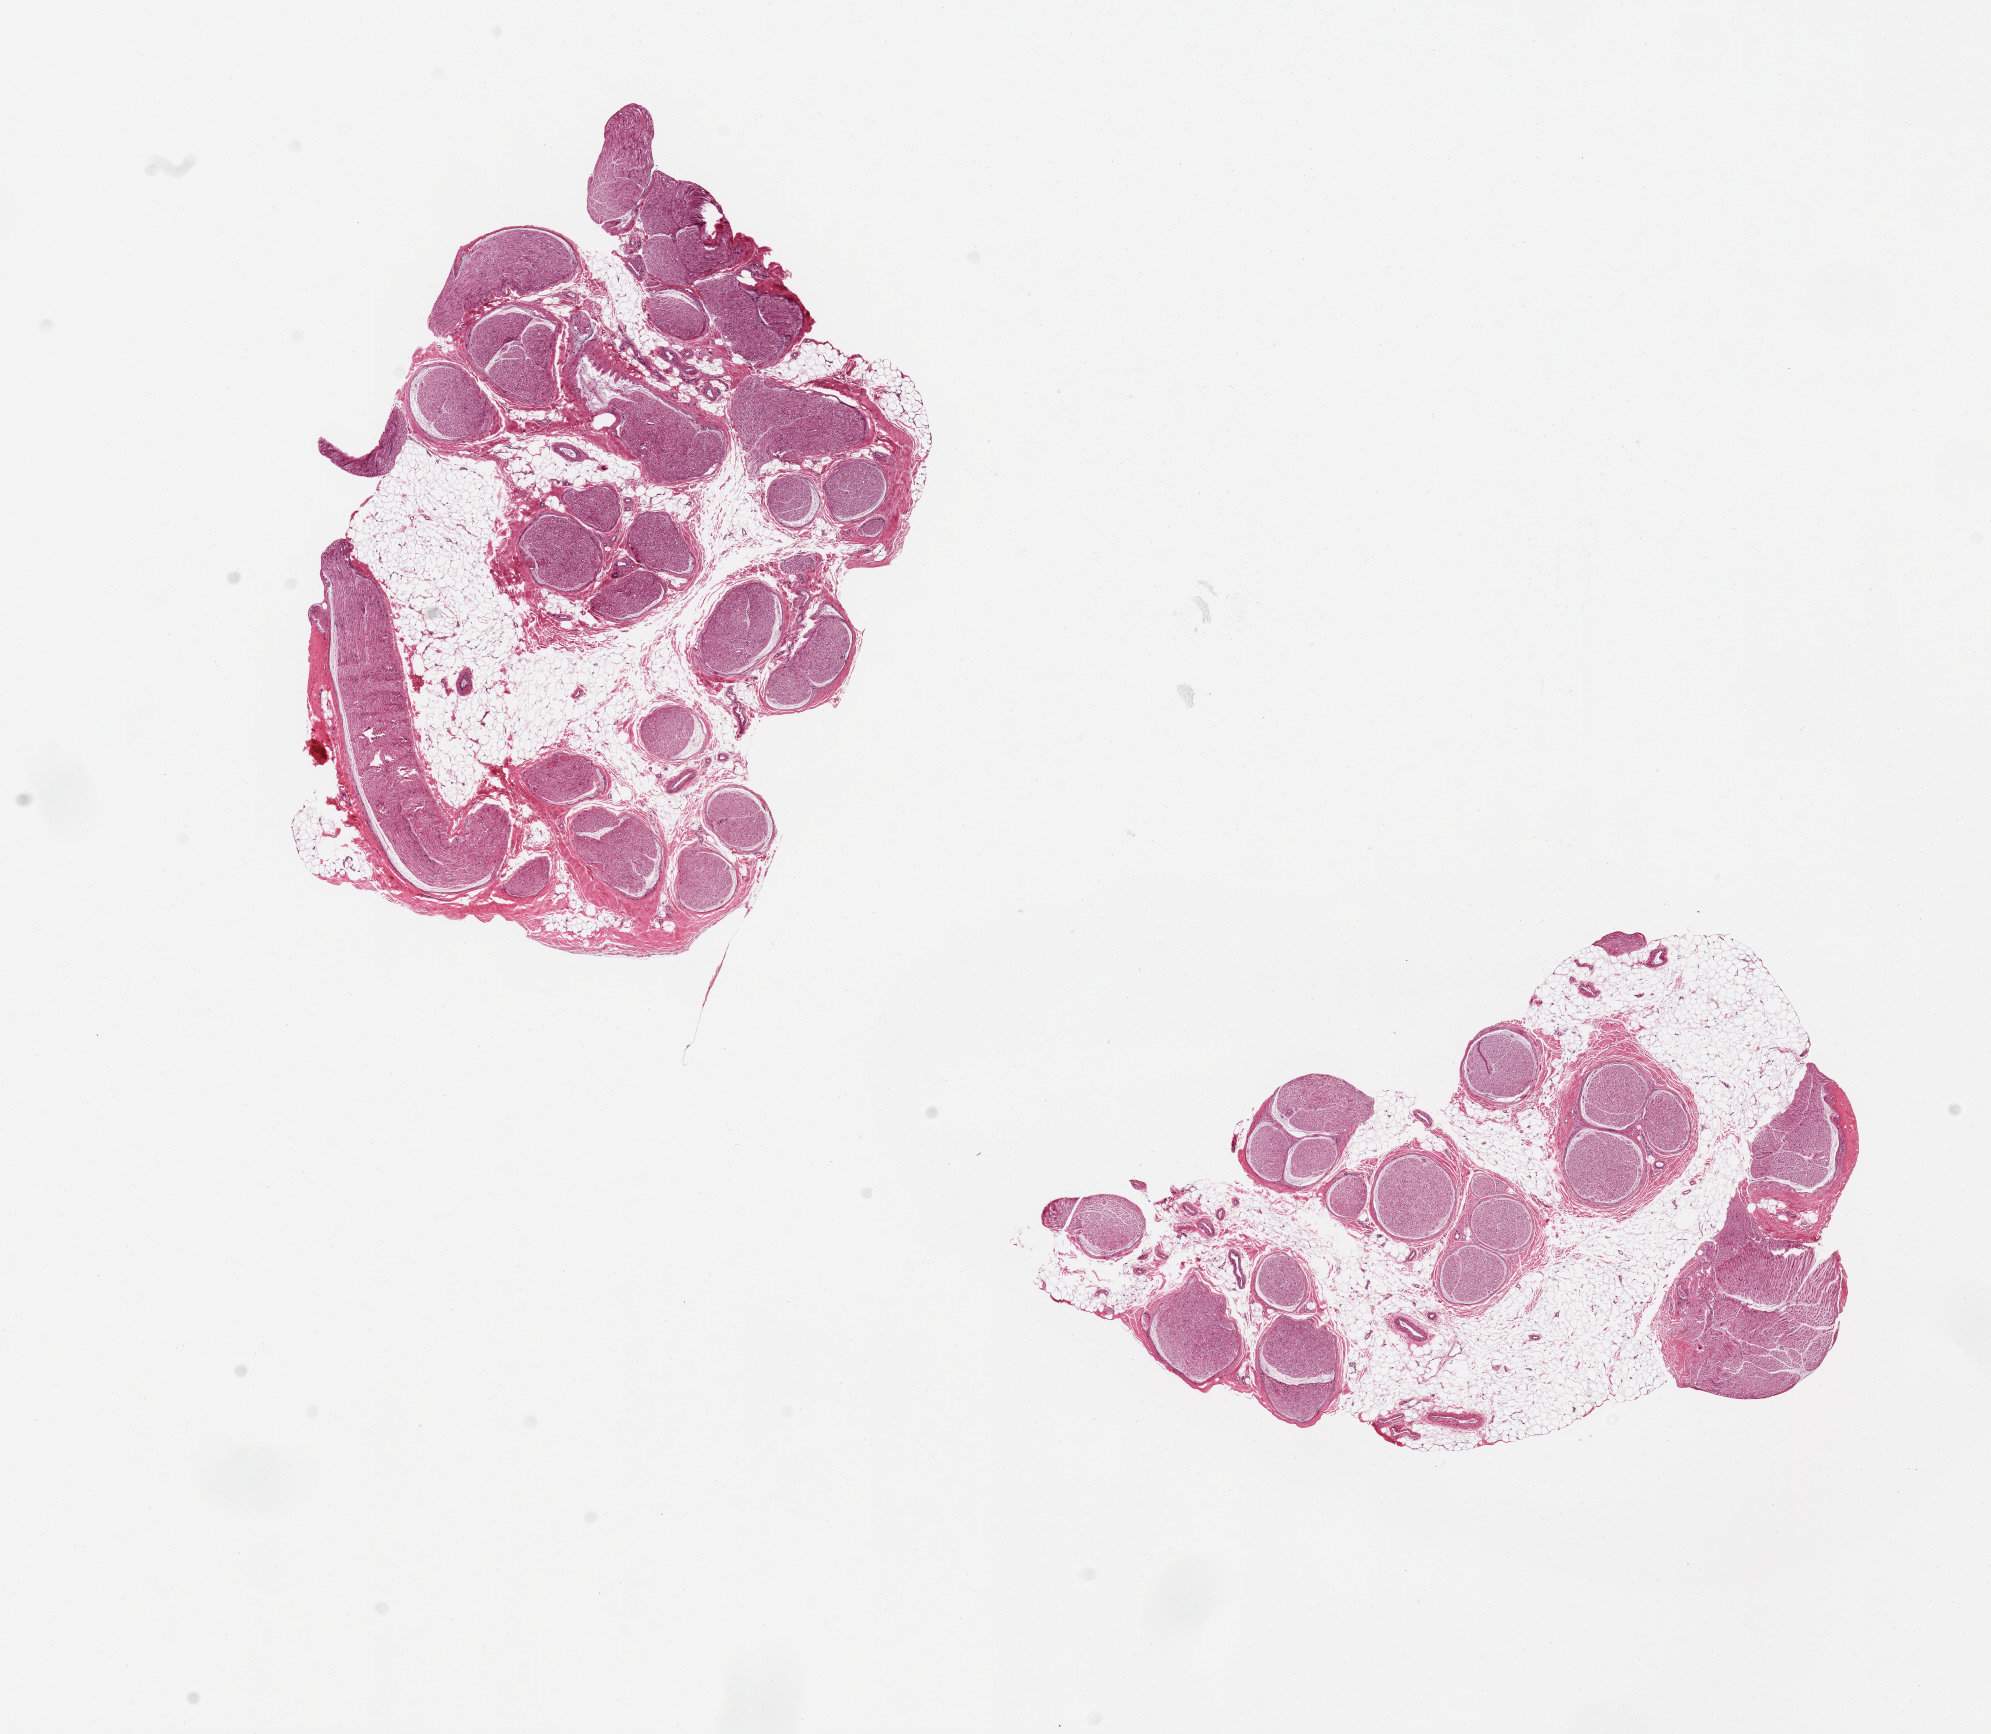
Whole-slide image, H&E stain, a low-resolution overview of the entire scanned area, about 15.8 x 13.7 mm. PAXgene-fixed paraffin-embedded (PFPE) section. Section of tibial nerve (target tissue). Tissue donor sample. Donor sex: male.
Reviewer comment on this tissue sample: 2 pieces, minimal adherent fat.